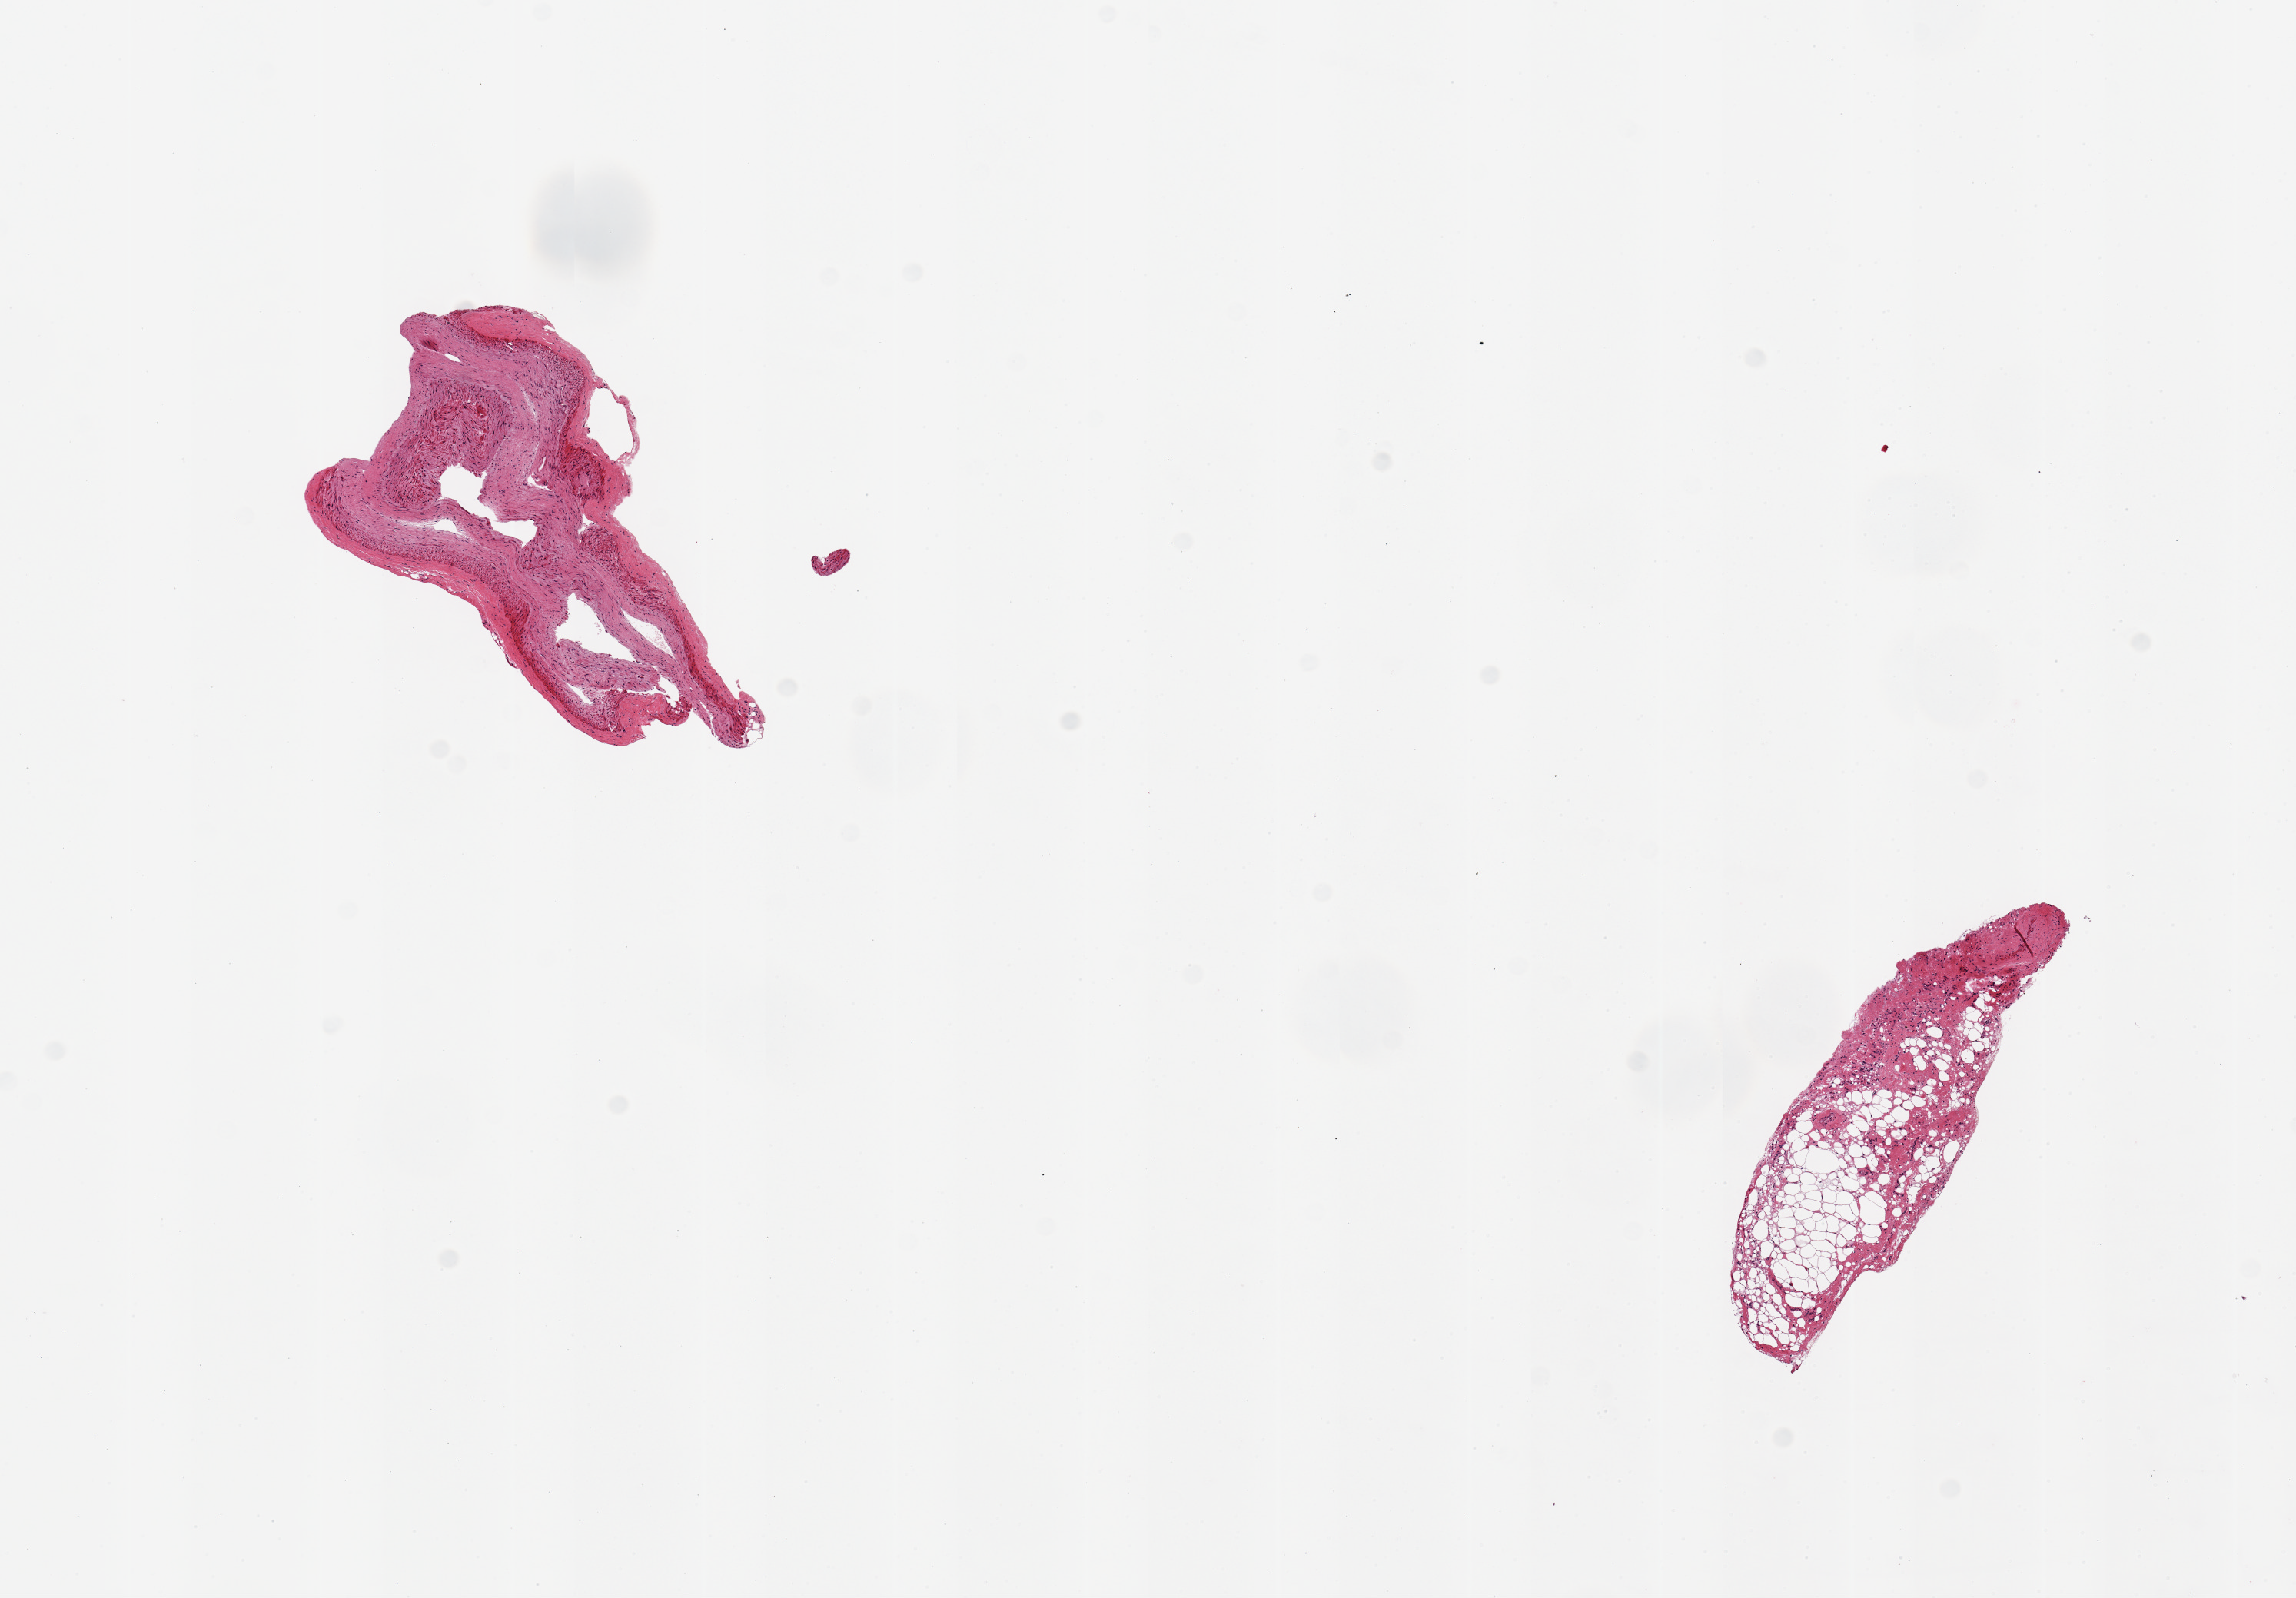
Whole-slide image, hematoxylin and eosin (H&E) stain, low-resolution overview of the scanned area, about 11.8 x 8.2 mm; PAXgene-fixed, paraffin-embedded tissue; target tissue: coronary artery; tissue donor sample. Donor sex: male.
Pathologist's review note for this sample: 2 pieces; 1 piece is vascular wall, second is moderately autolyzed fibroadipose tissue in this section.